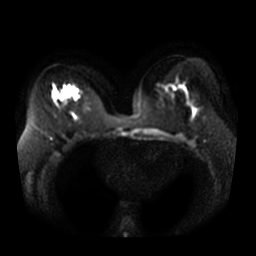
Breast MRI, one axial slice; position 20 of 36 along the scan axis; diffusion-weighted series; image 2 of 4 stored at this slice position (different b-values; order by instance number); 3 T; 5 mm slice thickness; 256 × 256 image matrix, field of view 370 × 370 mm. Female patient.
Annotated regions visible in this slice (manually delineated by an expert):
- tumour on diffusion-weighted imaging: box from (x=59, y=88) to (x=79, y=101) px